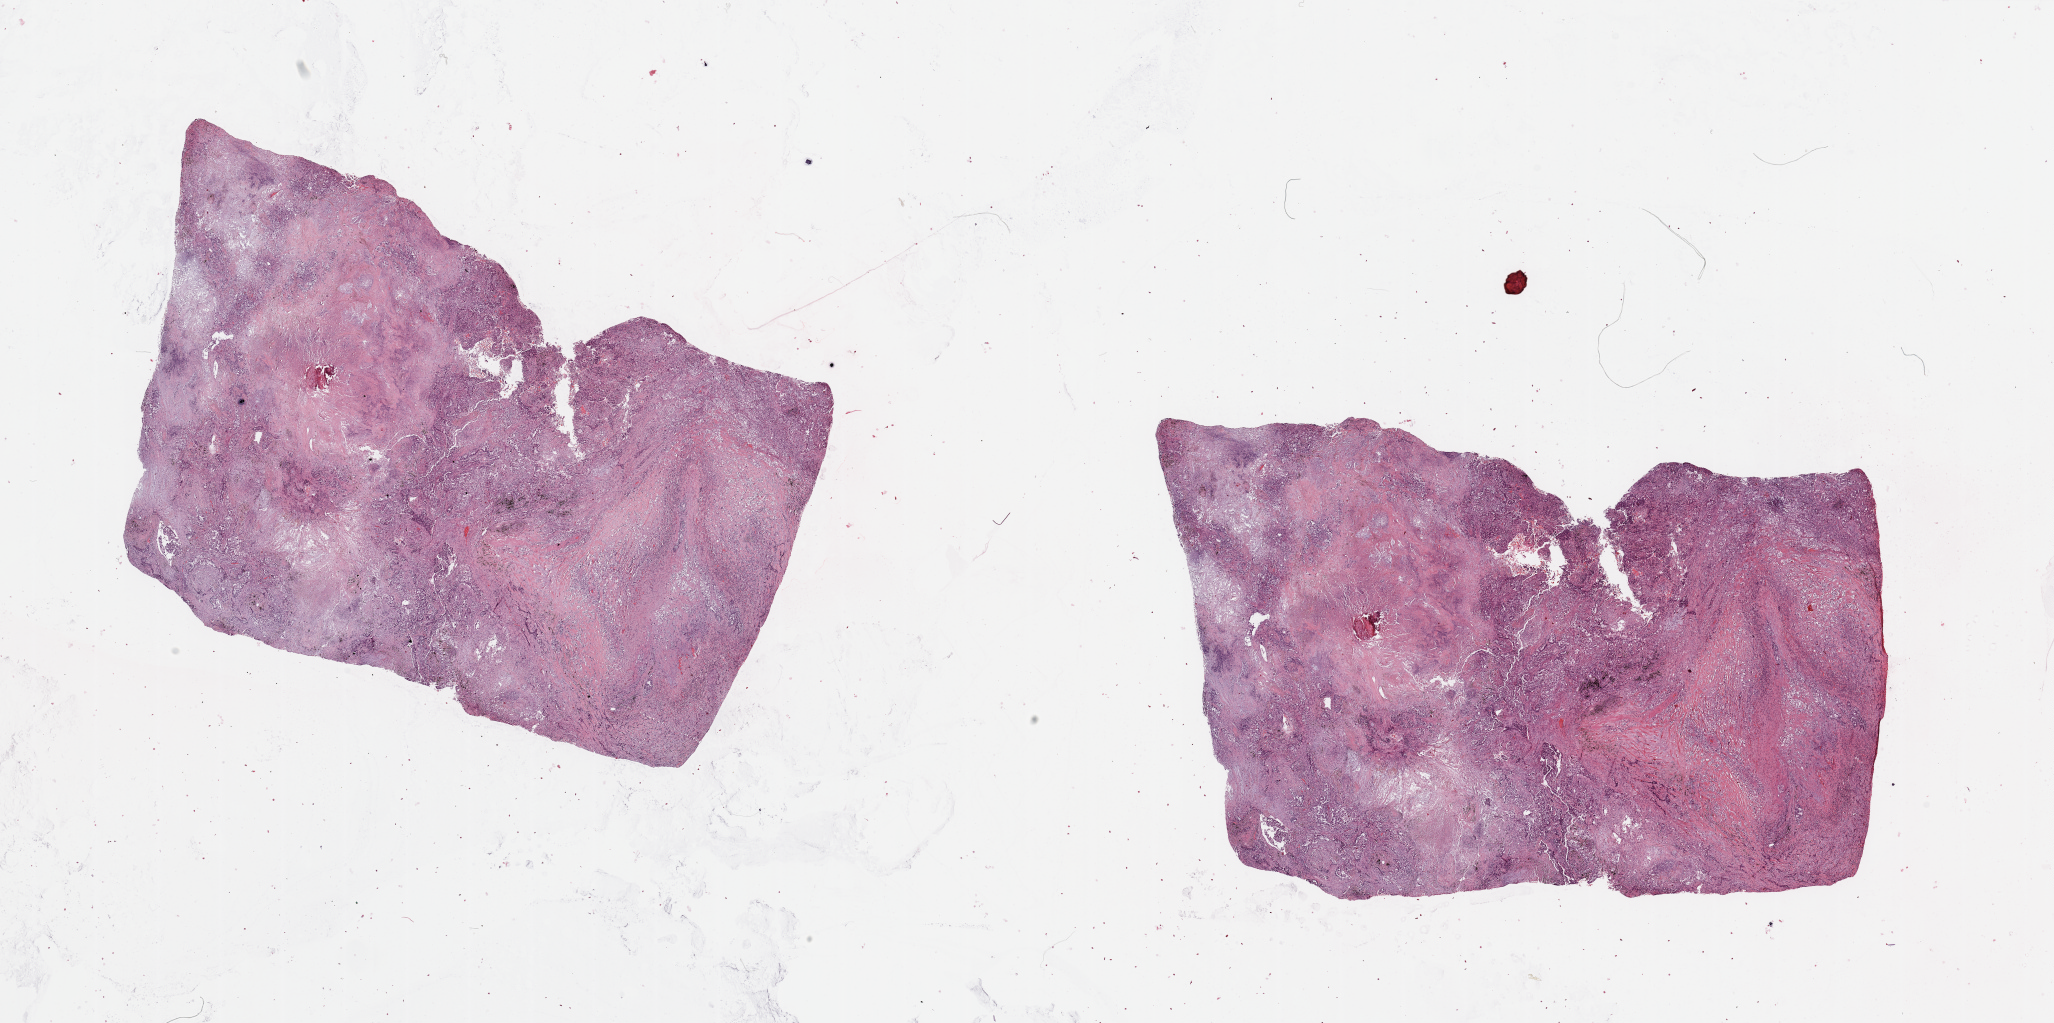
Digitized Hematoxylin and eosin (H&E) stained tissue section (whole slide) — whole scanned area (about 32.5 x 16.2 mm, slide scanned at 20x) shown as a low-resolution overview. Tumour tissue sample, lung. Male, 59 y/o.
Diagnosis: Adenocarcinoma, NOS.